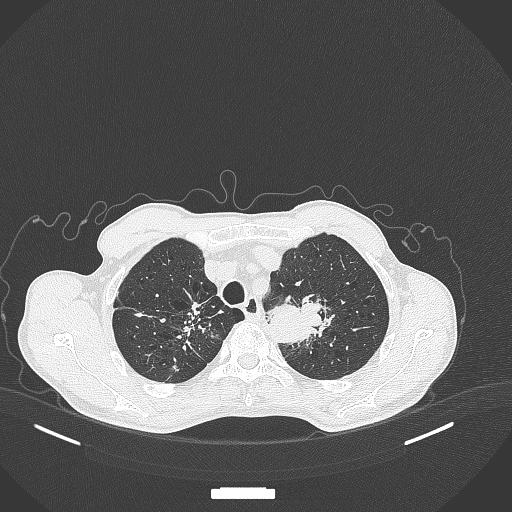
Chest CT, one axial slice; position 354 of 386 along the scan axis; reconstruction kernel B70f; lung window (W 1500 / L -600 HU); 1 mm slice thickness; 512 × 512 image matrix, field of view 400 × 400 mm. Male patient, age 65 years. Case-level facts recorded for this patient, not image findings: clinical TNM (as recorded): T2b N0 M0; histopathological grade: G2.
Structures marked on this image (rectangle marked by the reading radiologist):
- lung tumour (recorded histology: adenocarcinoma): bounding box (x1, y1, x2, y2) in pixels: (268, 293, 331, 346)